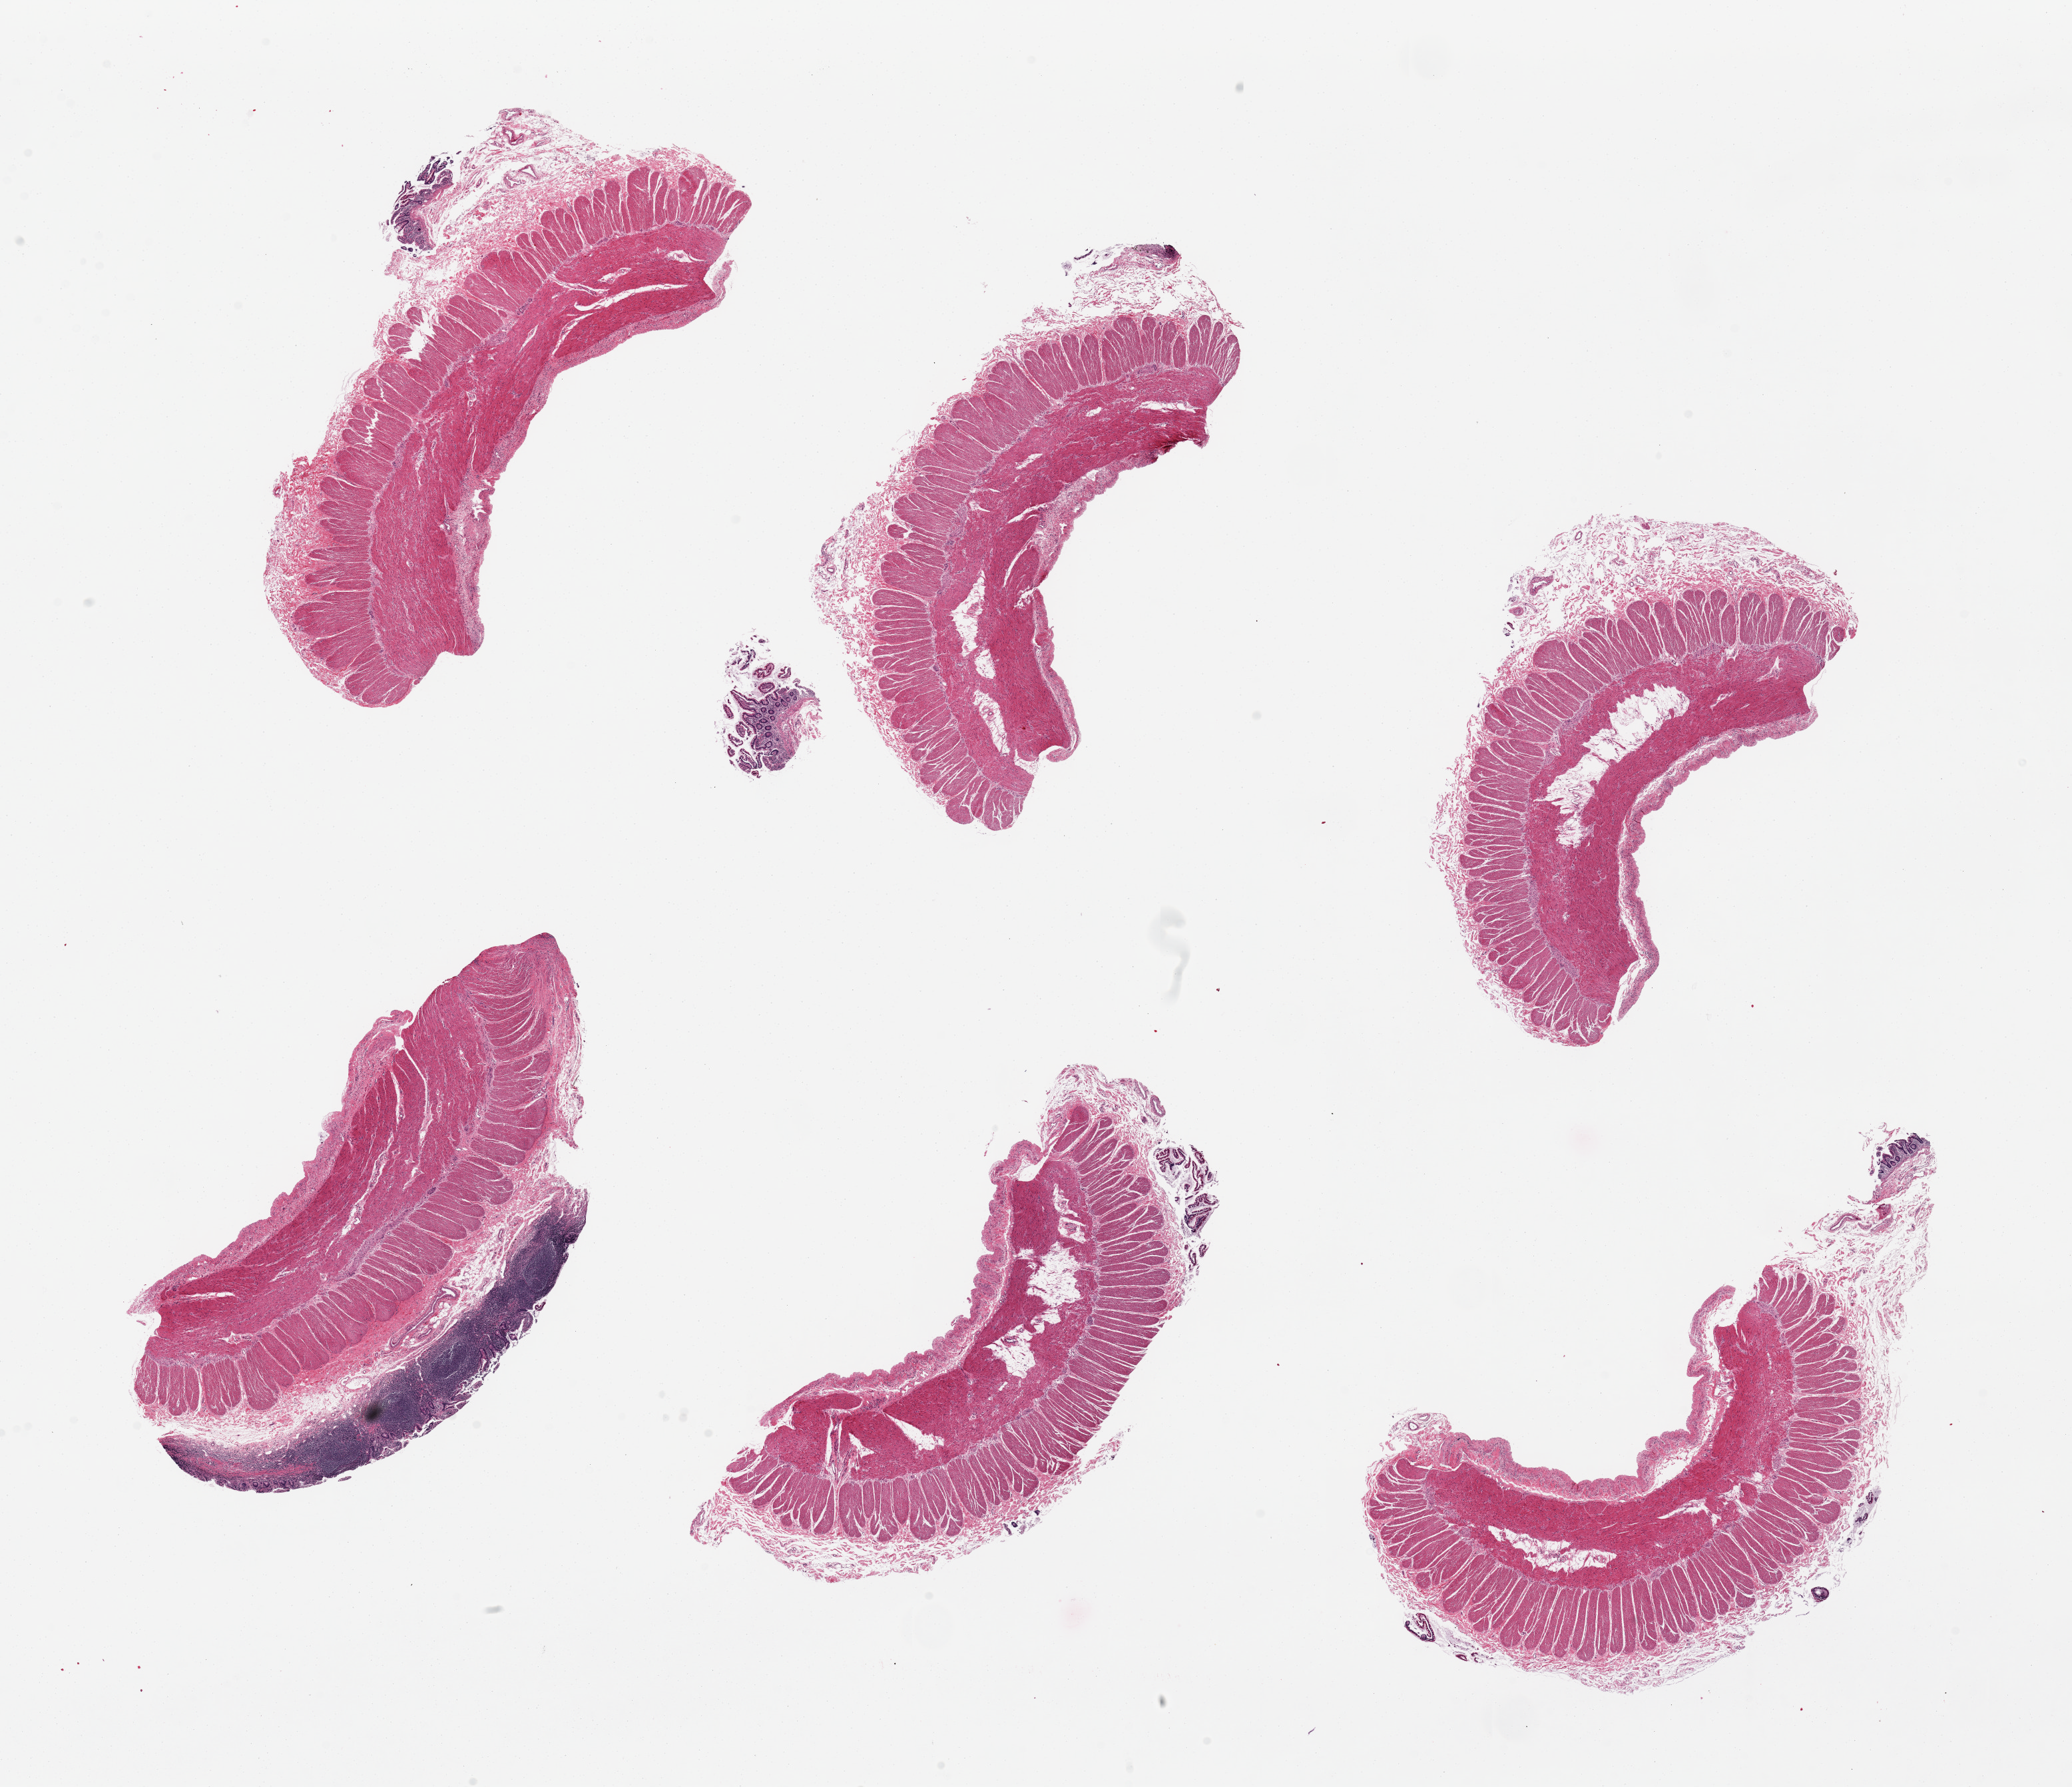
Whole-slide image, haematoxylin and eosin stain — low-resolution overview of the scanned area, about 24.6 x 21.2 mm (from a 20x scan), PAXgene-fixed paraffin-embedded (PFPE) section, target tissue: ileum, donor tissue sample.
Pathologist's review note for this sample: 6 pieces. up to 8x4mm; Only 1 of 6 has mucosa; all have muscularis propria. TARGET: Mucosa; discard muscularis. The one with mucosa has abundant lymphoid tissue.